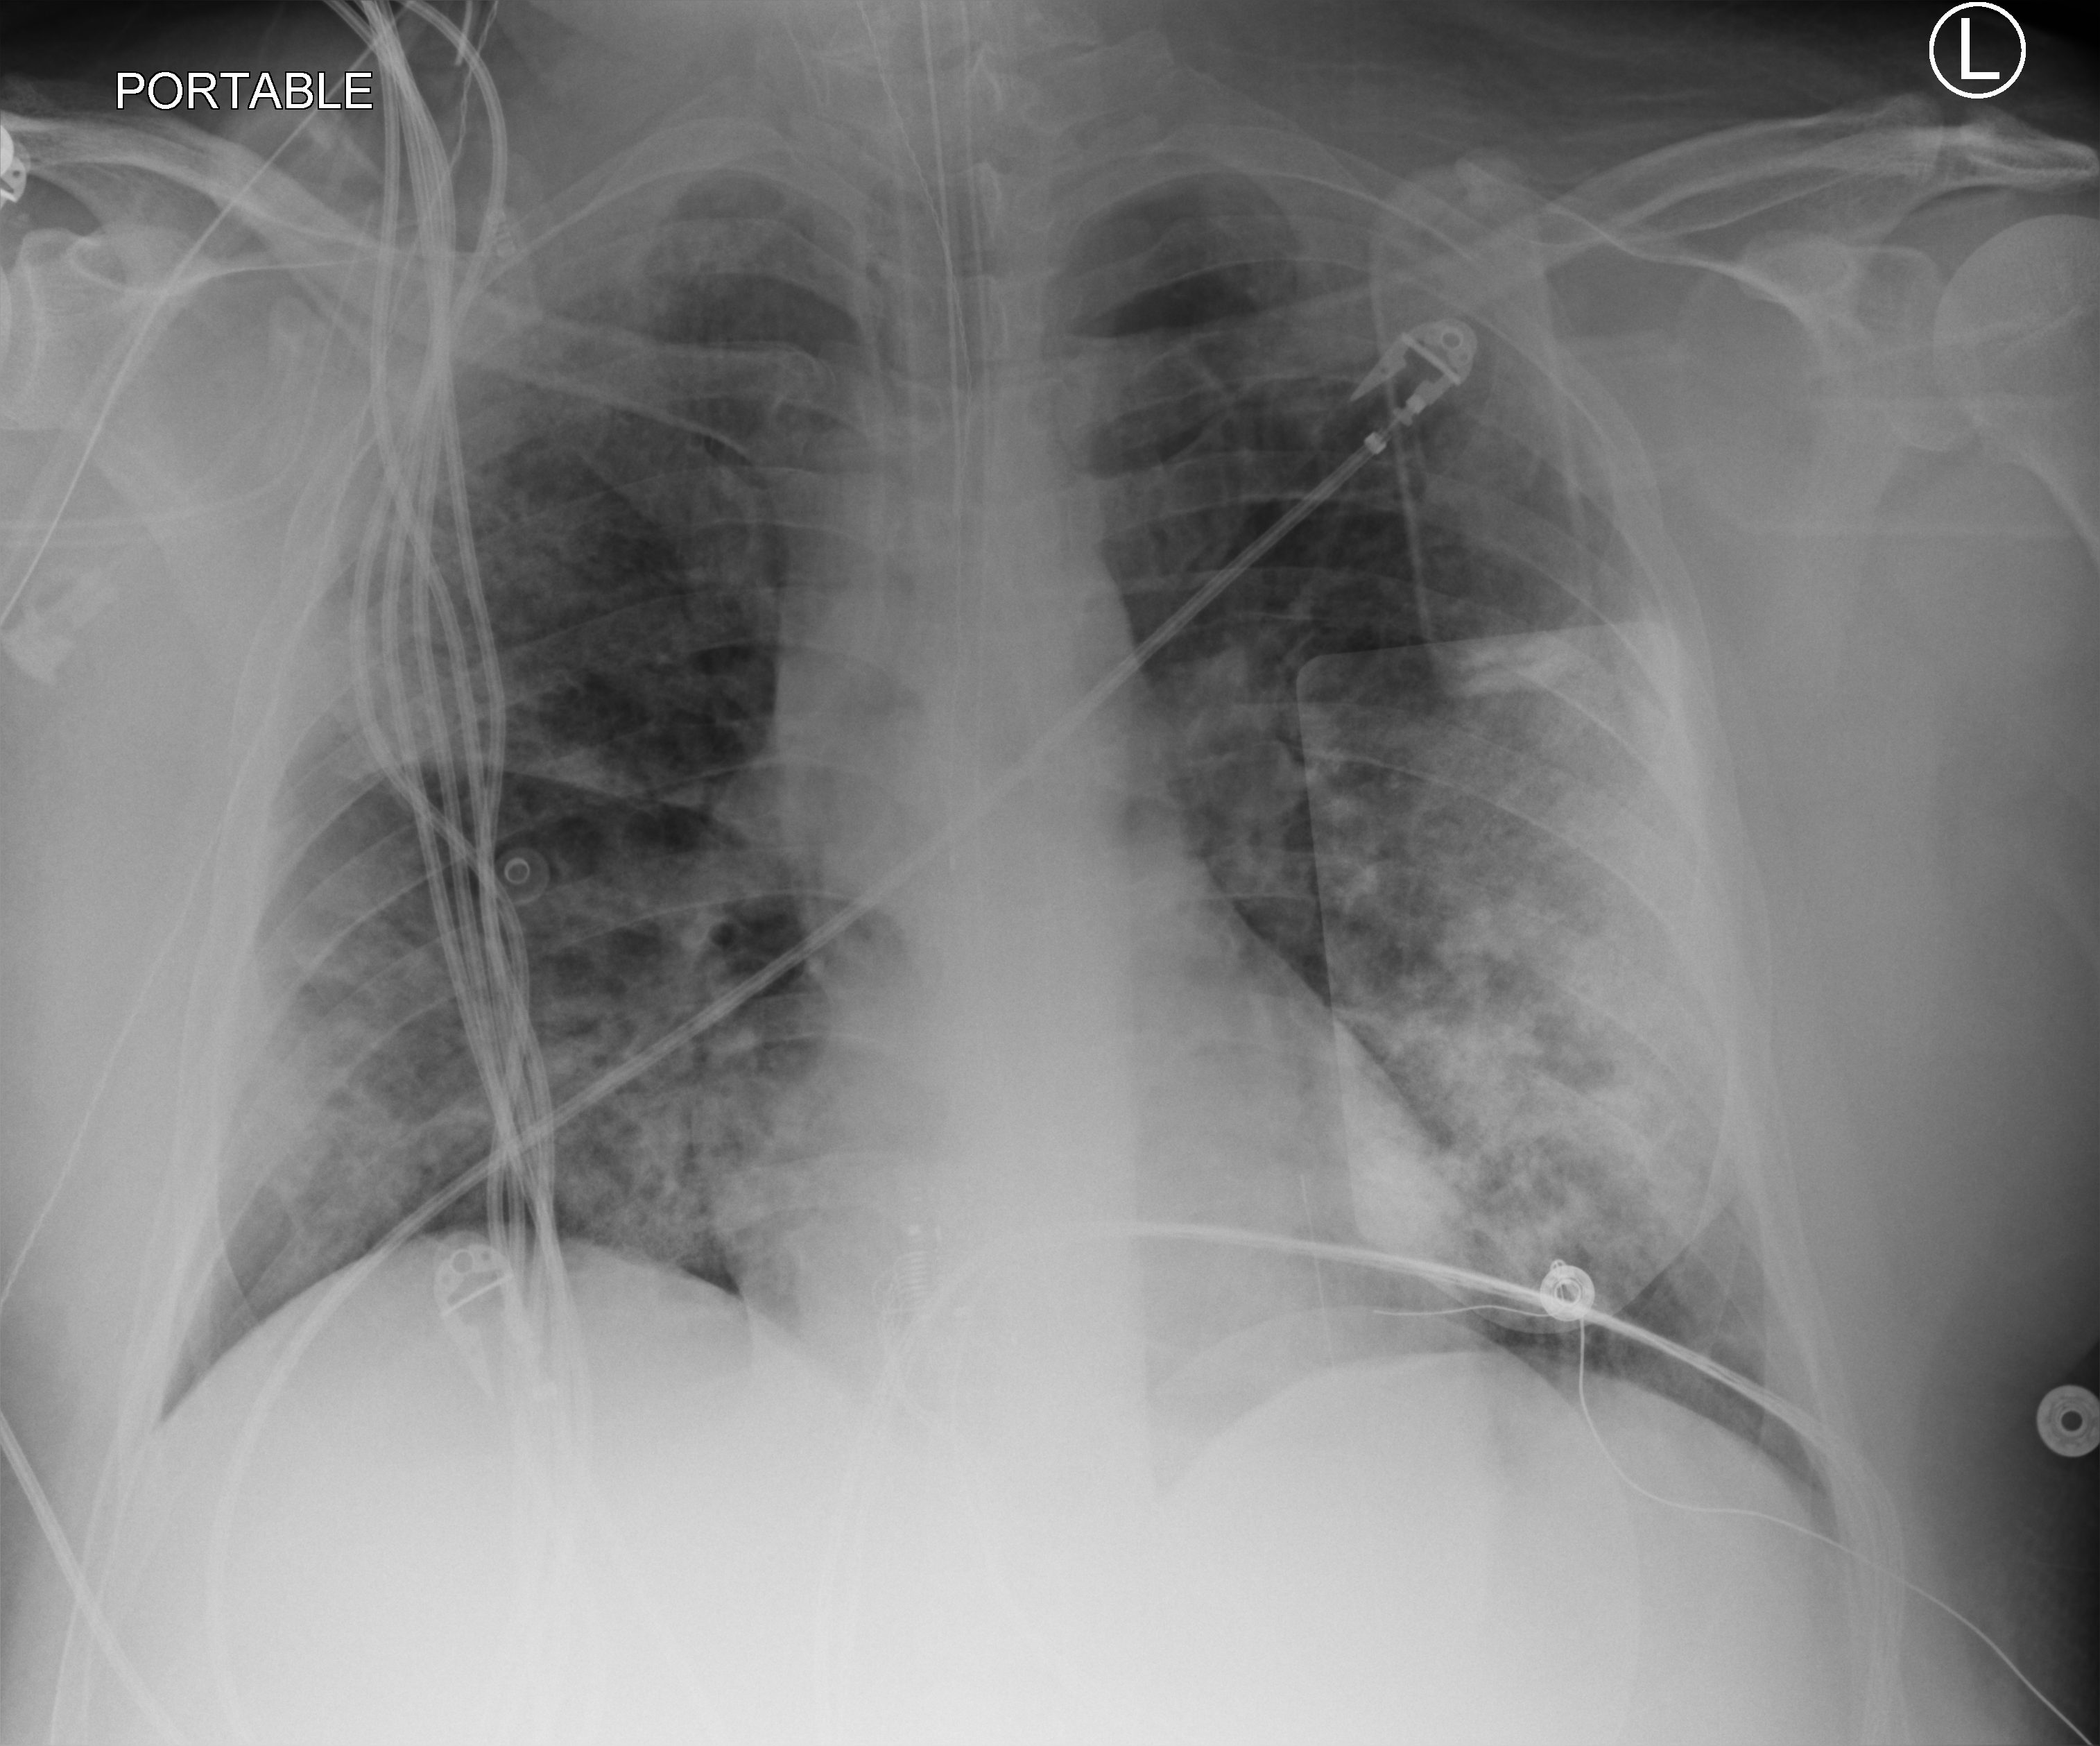
Bedside chest radiograph (computed radiography); anteroposterior (AP) projection. Adult patient hospitalised with COVID-19, age 18–59 years.
From the hospital-stay record, not from the radiograph (when in the stay this image was taken is not recorded): mechanically ventilated during this hospital stay: yes; admitted to intensive care during this hospital stay: yes; hypertension (admission record): yes.